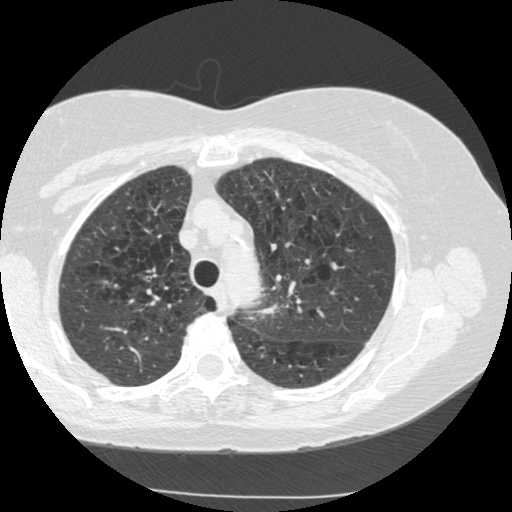
Low-dose screening chest CT, axial slice. Second annual screen. Lung window (W 1500 / L -600 HU). 1.25 mm slice thickness. Slice 197 of 249 in the series. Female participant, aged 70 years at enrolment. Current smoker at enrolment.
Lesion marked by an expert reader, box from (x=235, y=271) to (x=295, y=336) px. Screening reader's record for this exam (one nodule recorded; not confirmed to be the boxed lesion): non-calcified nodule or mass ≥4 mm, left upper lobe, 15 × 13 mm, spiculated (stellate) margins, soft tissue attenuation, pre-existing on the prior screen: yes; interval growth: yes. Lung cancer was diagnosed 360 days after this screen (after the third annual screen): neoplasm, malignant, left upper lobe, stage IIIB (AJCC 6th edition), 40 mm at pathology.